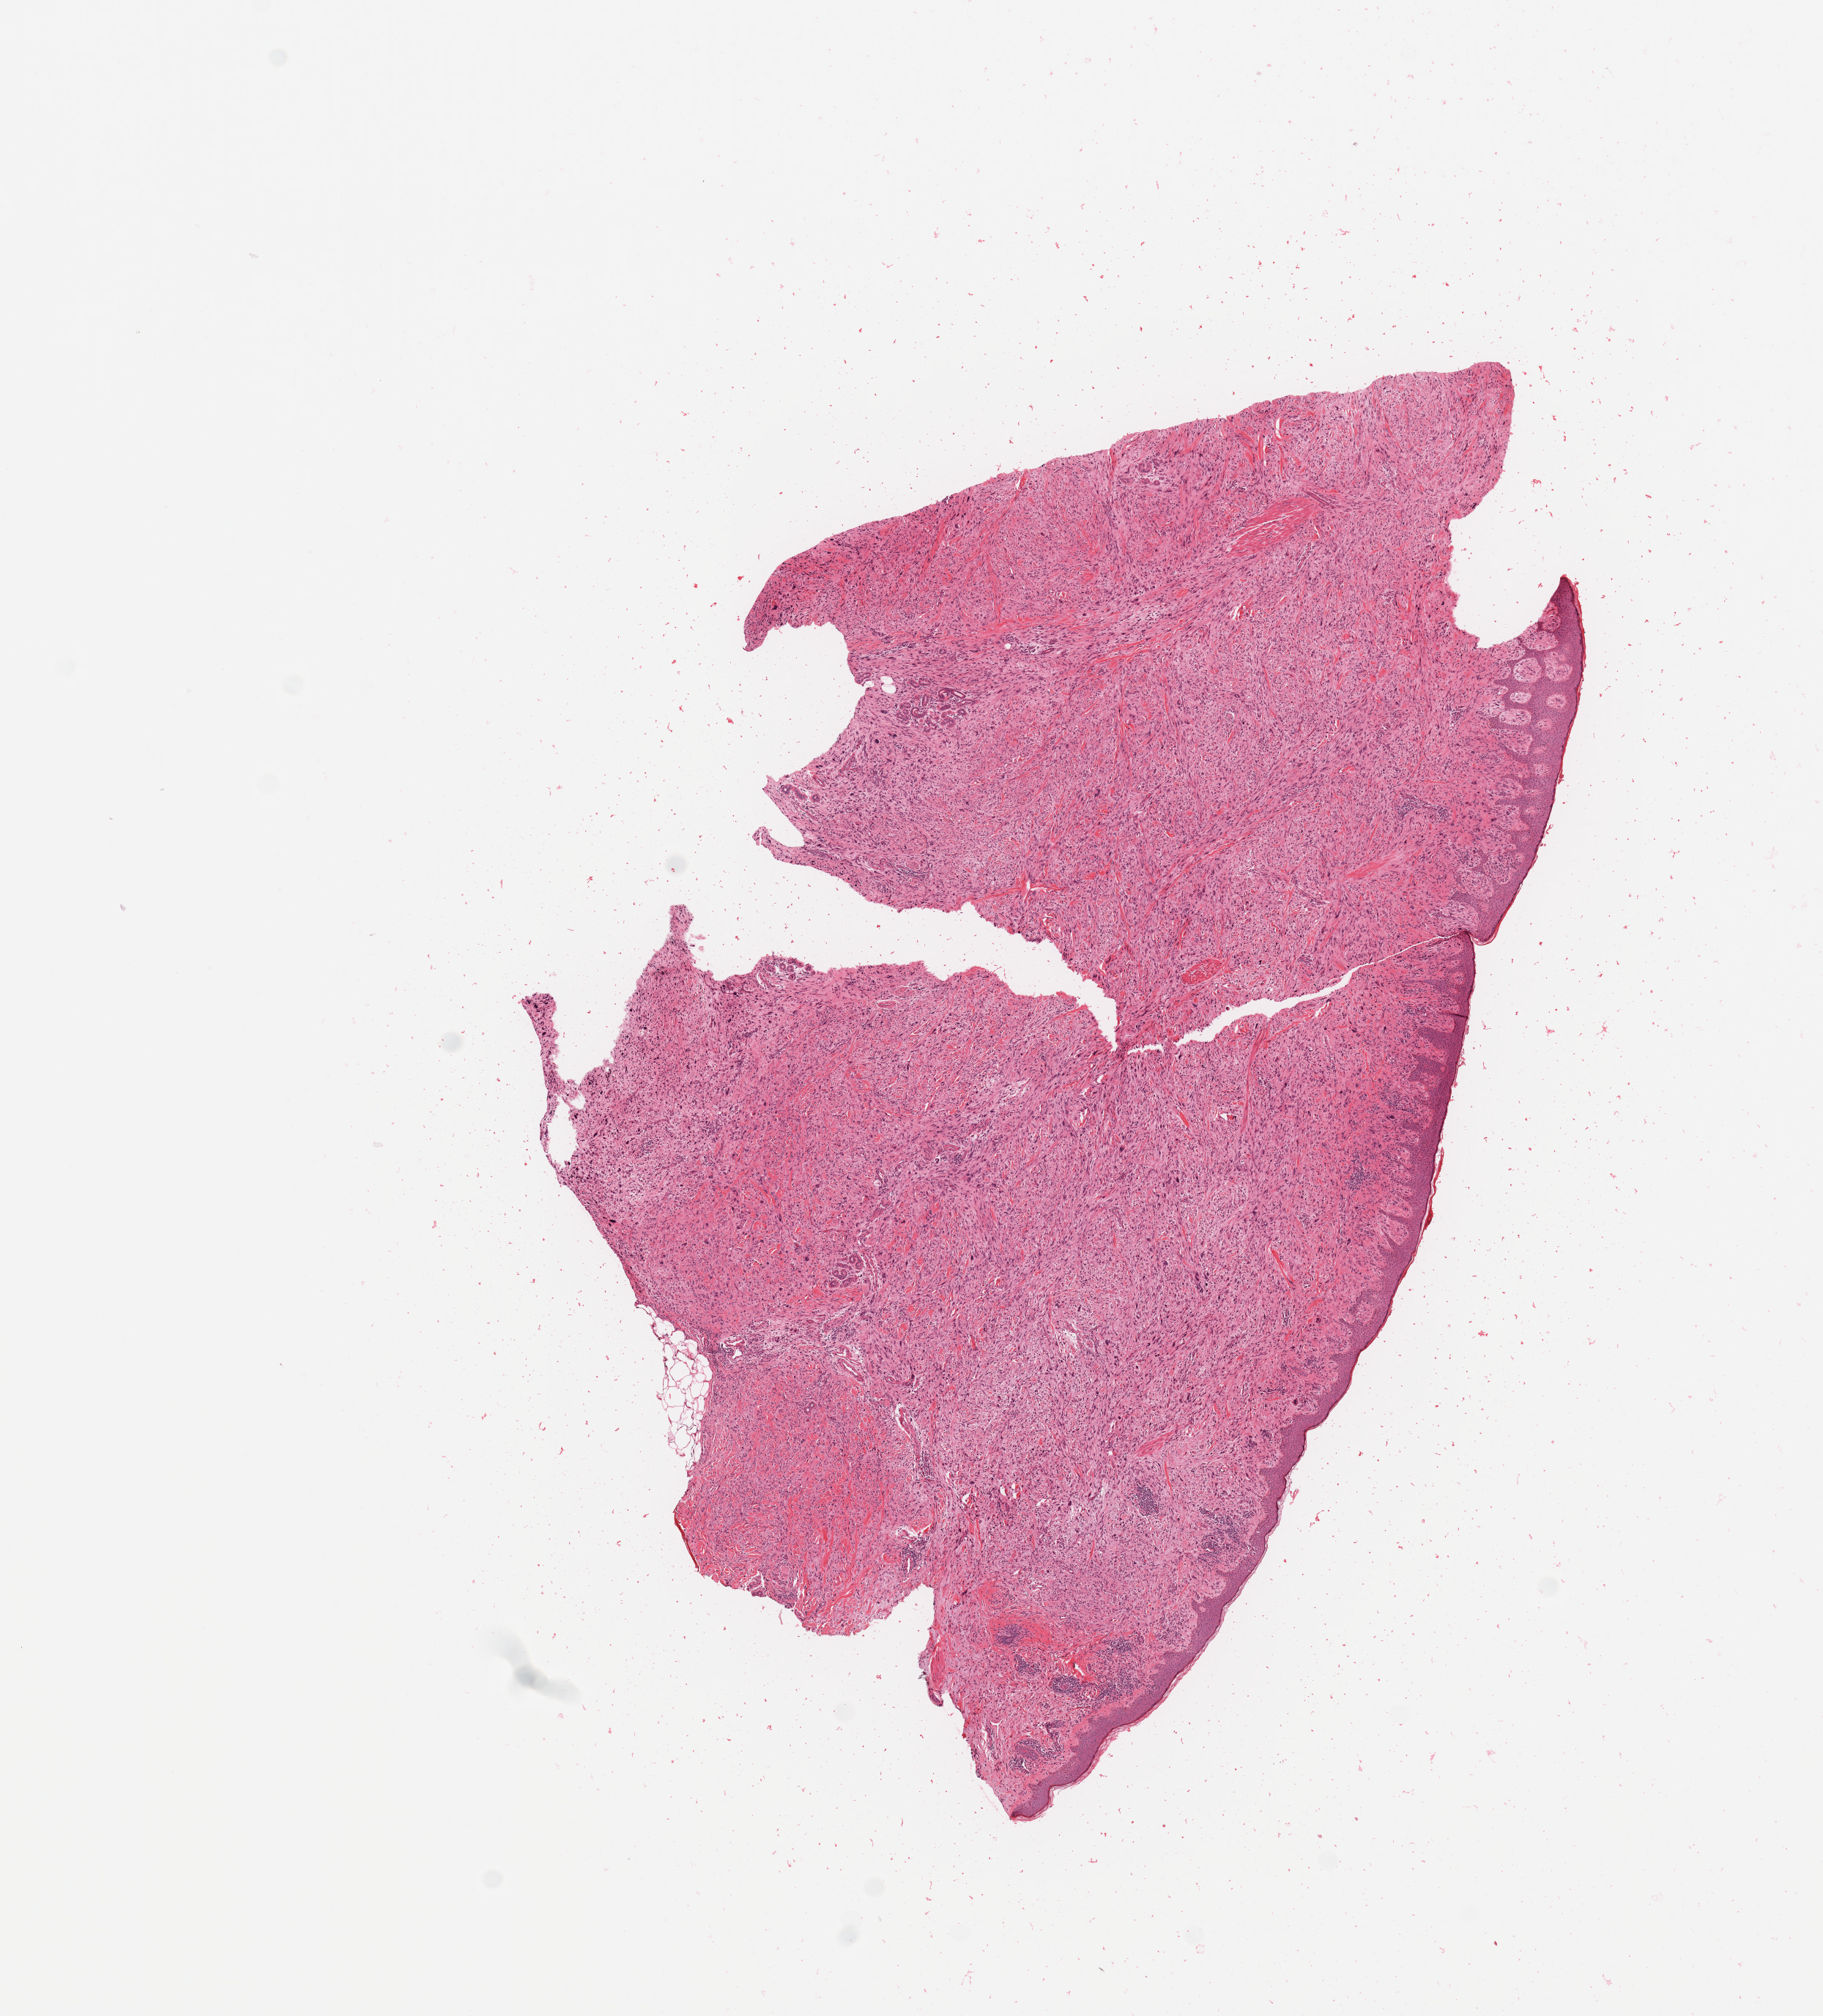
H&E whole-slide image — low-resolution overview of the scanned area, about 9.8 x 10.9 mm (from a 20x scan); tumour tissue sample. Female patient.
- primary tumour site (as recorded): upper extremity
- patient diagnosis (cohort enrolment): sarcoma (site not recorded at cohort level)